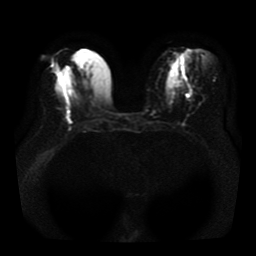
Breast MRI, one axial slice; slice 15 of 41 in the series (ordered by position); diffusion-weighted series; image 2 of 4 stored at this slice position (different b-values; order by instance number); 1.5 T; 5 mm slice thickness; 256 × 256 image matrix. Female patient.
Annotated regions visible in this slice (expert manual segmentation):
- tumour on diffusion-weighted imaging: bounding box <67,113,71,117> (left, top, right, bottom; pixels)